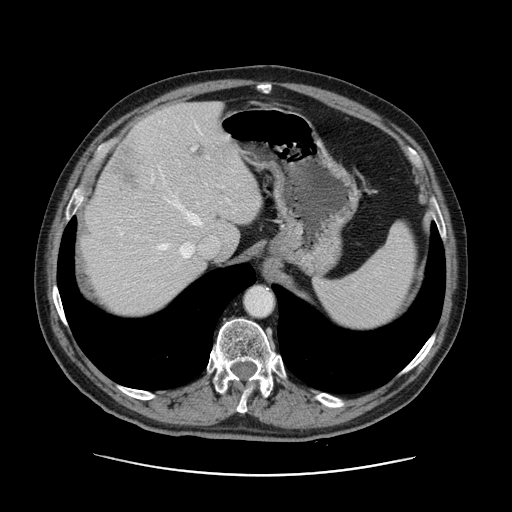
Contrast-enhanced abdominal CT, one axial slice. Slice 98 of 141 in the series (ordered by position). 120 kVp. Intravenous contrast given. Soft-tissue window (W 400 / L 40 HU). 2.5 mm slice thickness. 512 × 512 image matrix. Male patient, age 72 years. From the clinical record (not read from this slice): diagnosis: colorectal cancer liver metastases, imaged before liver resection; multiple liver metastases: yes; largest metastasis: 5.4 cm.
Annotated regions visible in this slice (outlined manually by an expert reader):
- hepatic veins: box from (x=121, y=126) to (x=209, y=258) px
- liver: (x=81, y=102)–(x=262, y=318)
- planned liver remnant (the part of the liver to remain after resection): (x=84, y=102)–(x=262, y=318)
- portal vein (with intrahepatic branches): (x=182, y=147)–(x=229, y=255)
- liver metastasis: (x=107, y=145)–(x=141, y=192)